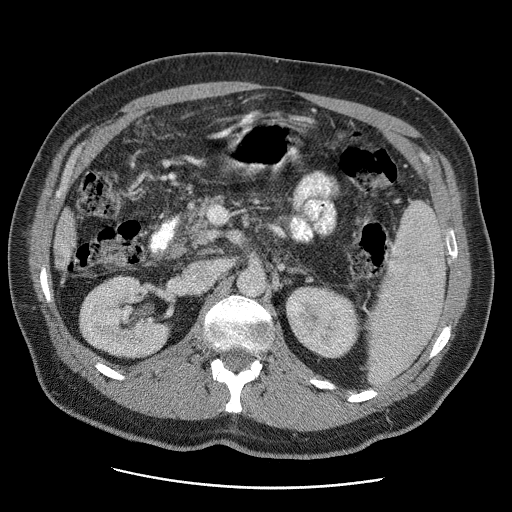
Contrast-enhanced abdominal CT (liver protocol), one axial slice; slice 9 of 81 in the series (ordered by position); 120 kVp; soft-tissue window (W 400 / L 40 HU); 2.5 mm slice thickness; 512 × 512 image matrix. From the clinical record (not read from this slice): diagnosis: hepatocellular carcinoma (patient treated with transarterial chemoembolisation; whether this scan precedes or follows treatment is not stated here); TNM stage (as recorded): Stage-IIIA; Child-Pugh class: A; tumour differentiation: moderately differentiated.
Outlined on this slice (semi-automatic segmentation, software-assisted and operator-edited):
- liver parenchyma outside the tumour (the mass and vessels are separate outlines, so this box may not span the whole liver): bounding box <54,210,76,270> (left, top, right, bottom; pixels)